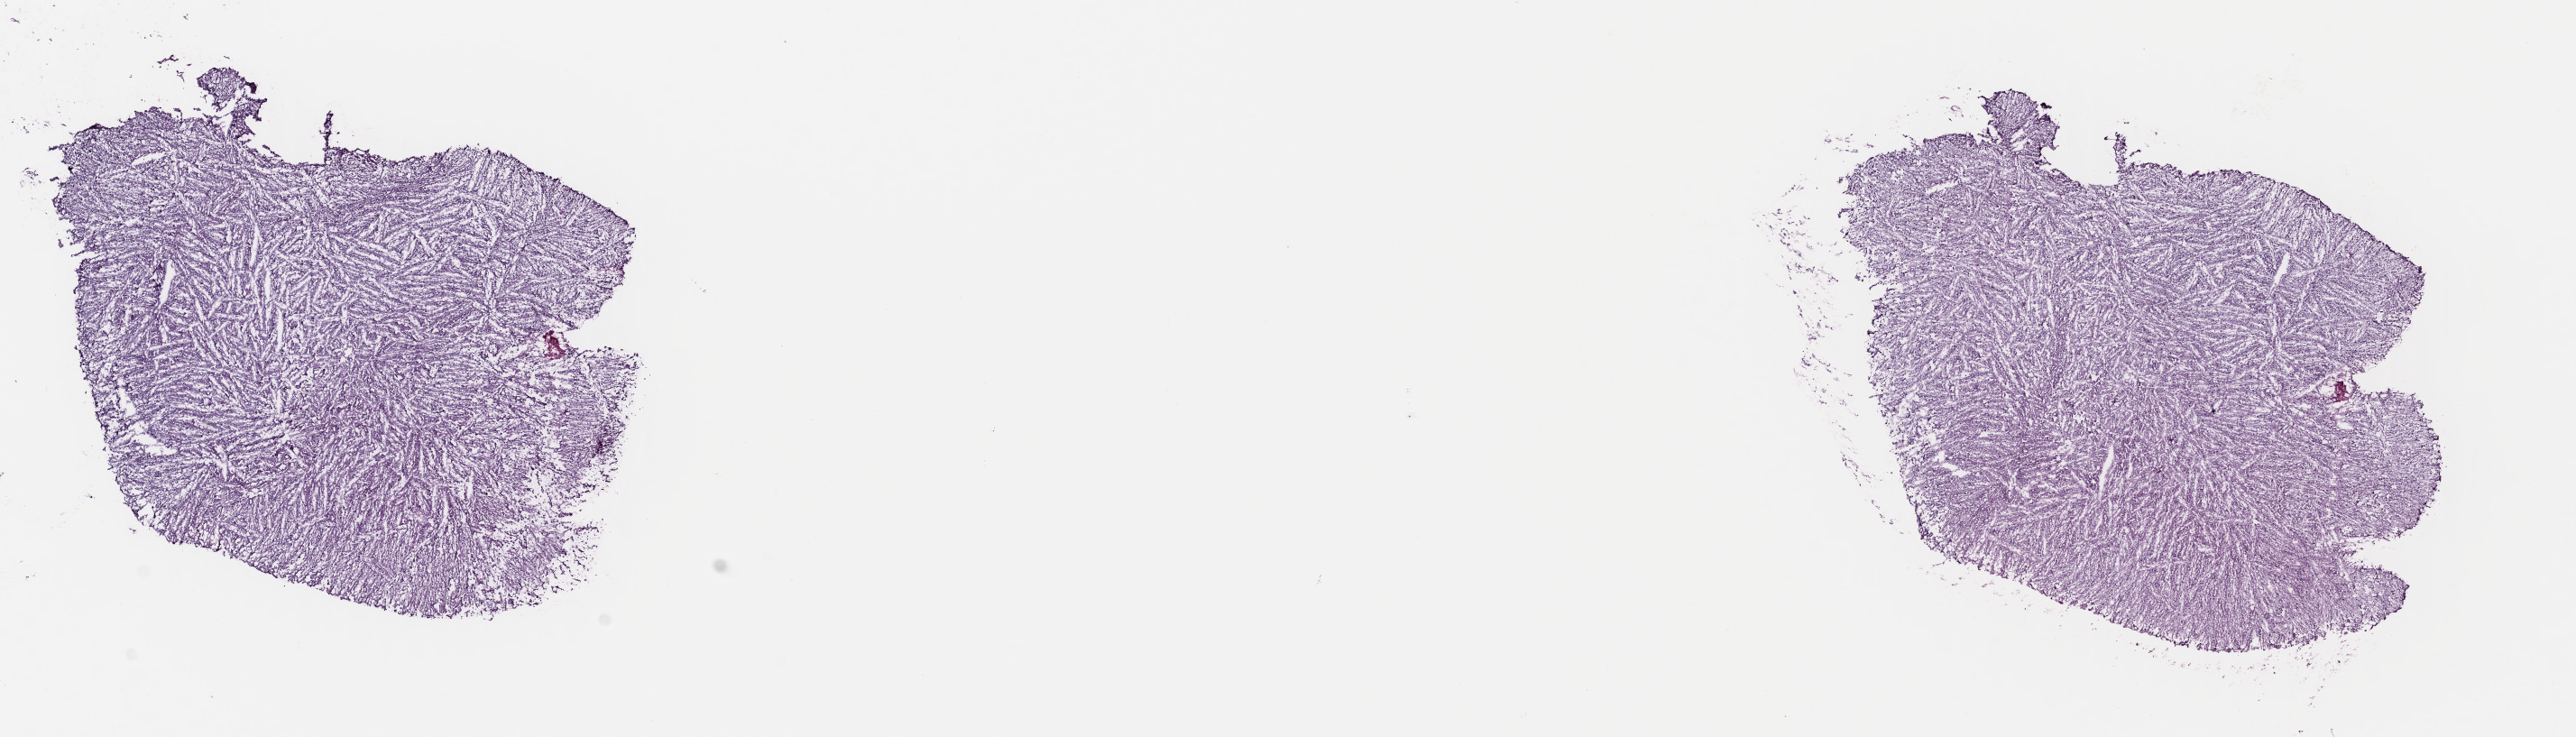
Digitized Hematoxylin and eosin (H&E) stained tissue section (whole slide) — shown as a low-resolution overview of the whole scanned area (about 22.4 x 6.4 mm, slide scanned at 40x); frozen section; sample: primary tumour, brain. Male, age 50 years at initial diagnosis. Histologic grade: G2 (moderately differentiated). Pathologist review of this section (percent, as recorded): tumour cells 60%, tumour nuclei 80%, normal cells 10%, stromal cells 30%, necrosis 0%. Inflammatory infiltration, as recorded: lymphocyte infiltration 0%, monocyte infiltration 0%, neutrophil infiltration 0%.
Diagnosis: Oligodendroglioma, NOS (cerebrum). Laterality: left.